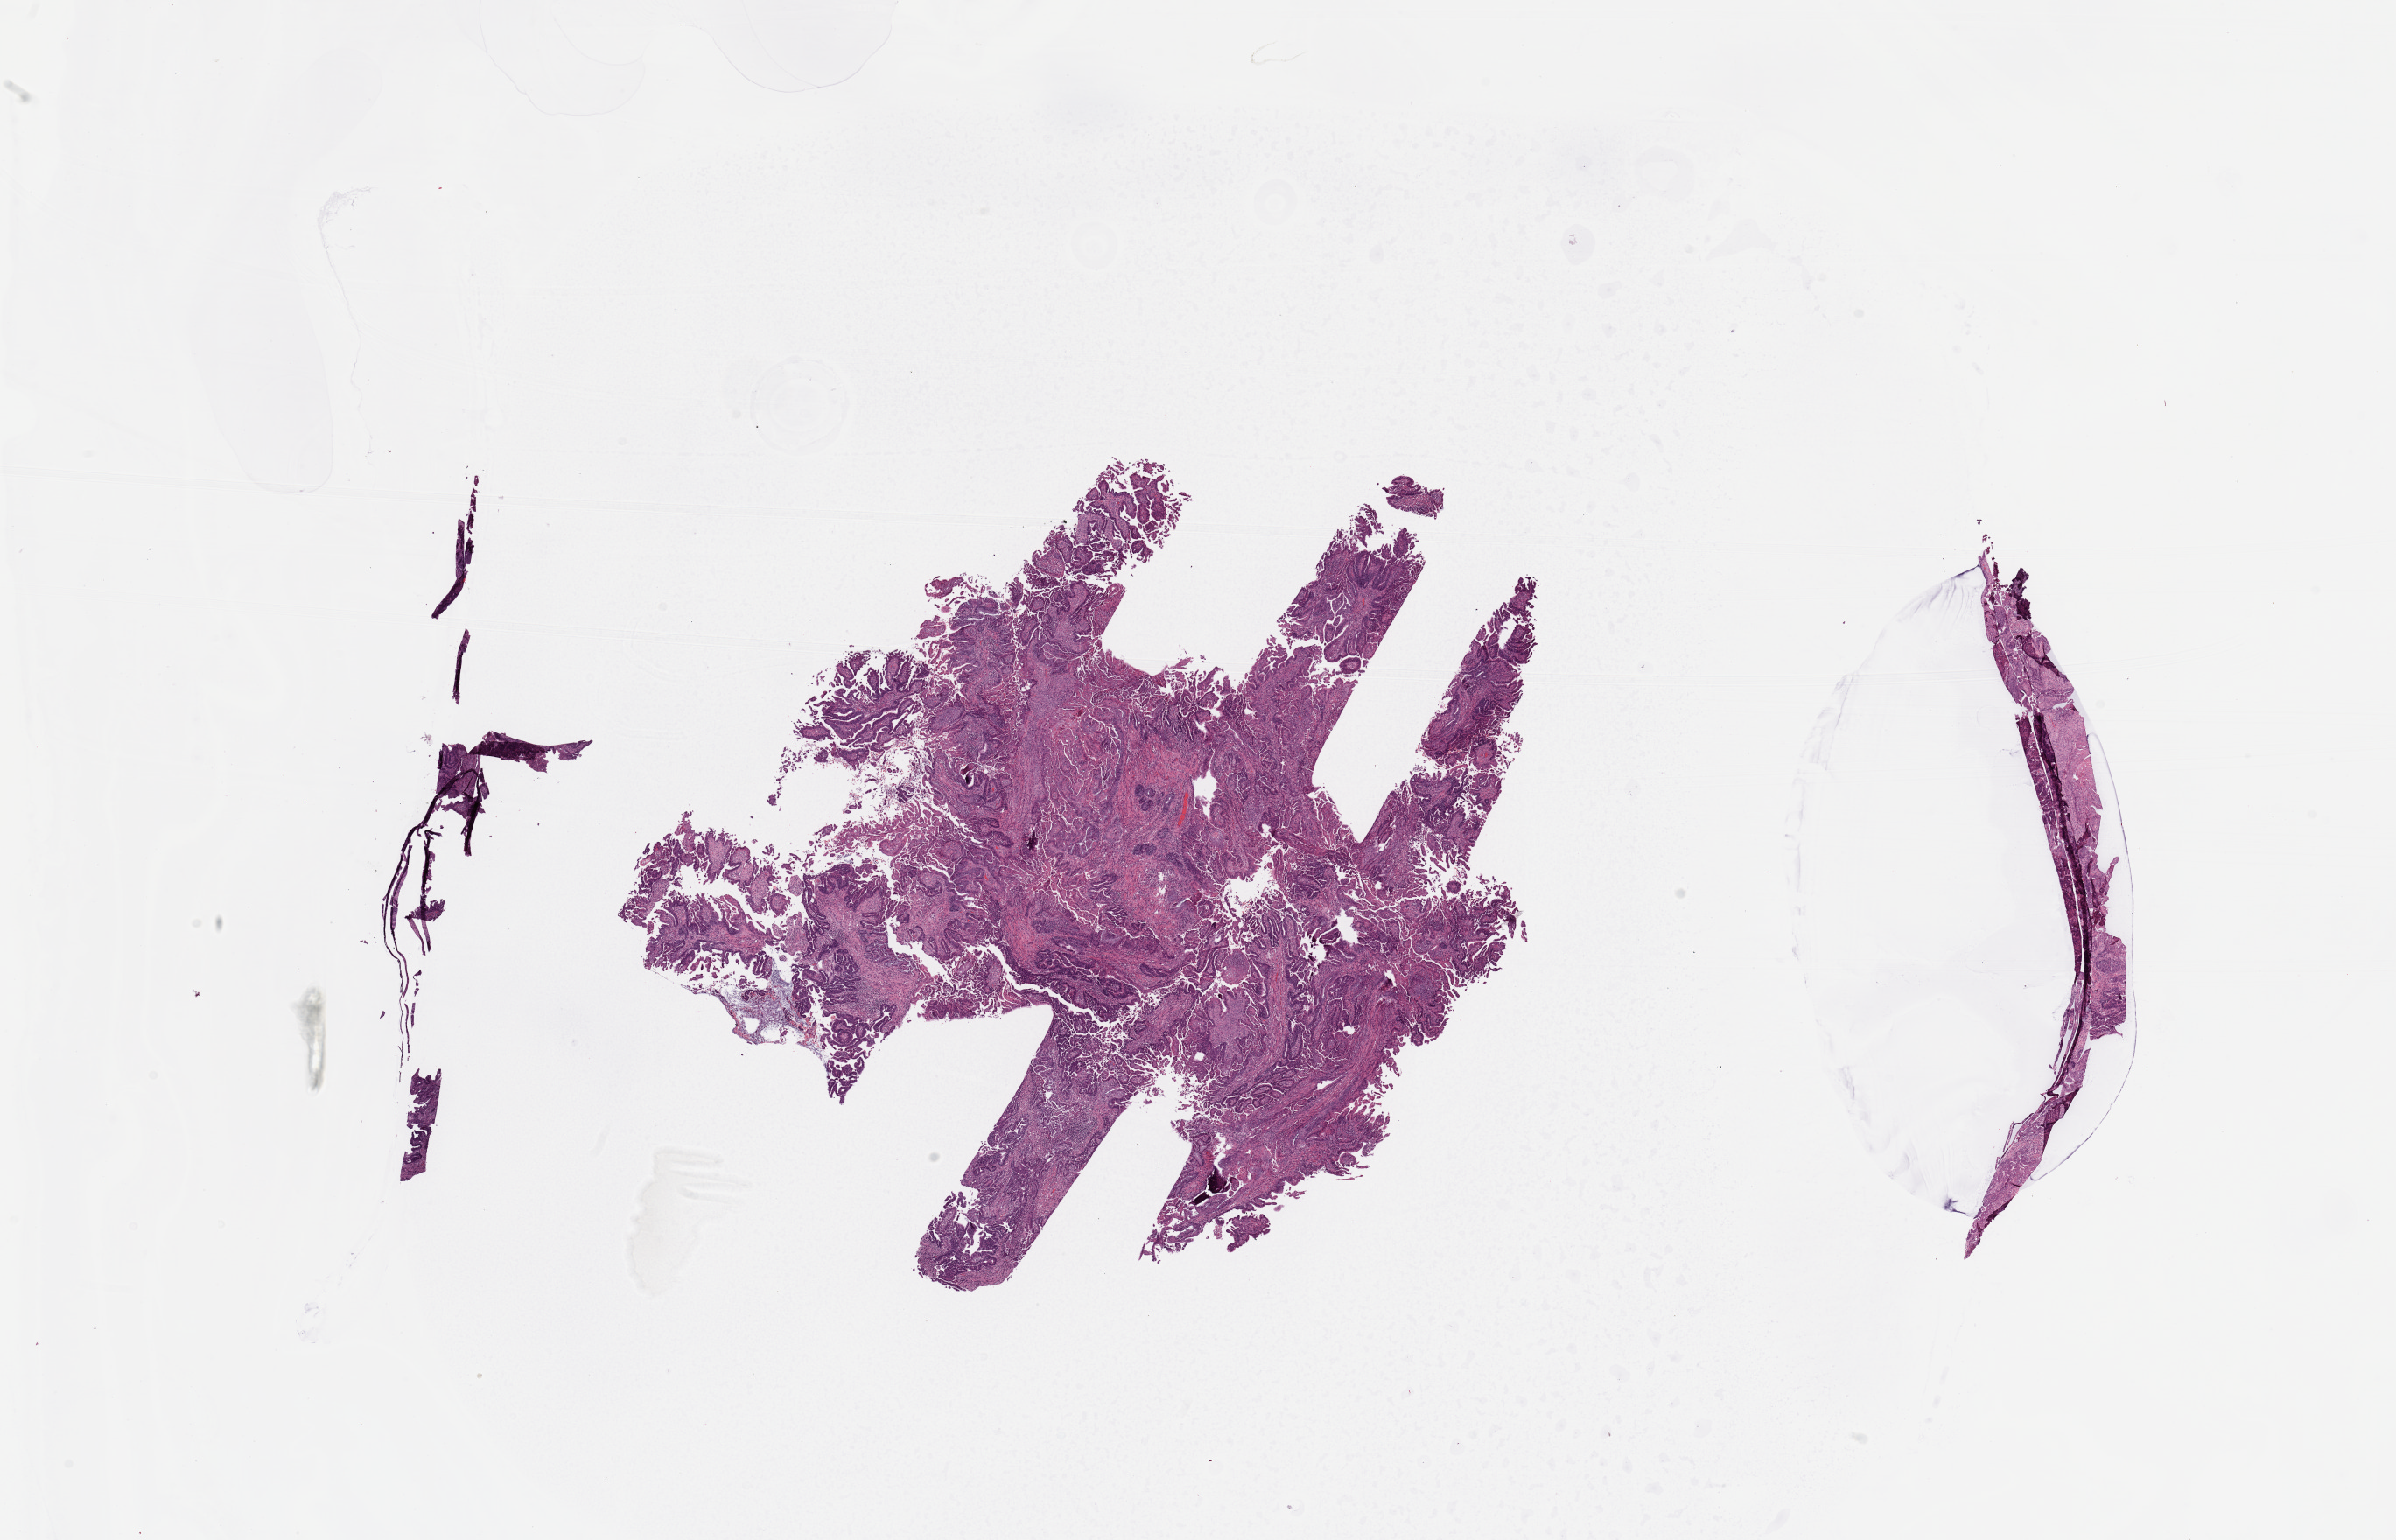
Digitized H&E-stained tissue section (whole slide) — shown as a low-resolution overview of the whole scanned area (about 21.7 x 13.9 mm, slide scanned at 20x), tumour tissue sample, sampled site: uterus. Patient: female, age 46 years. Histologic grade: G2 (moderately differentiated). Pathologist review of this section (percent, as recorded): tumour nuclei 80%, necrosis 2%.
Diagnosis: Endometrioid adenocarcinoma, NOS. AJCC pathologic stage: I.